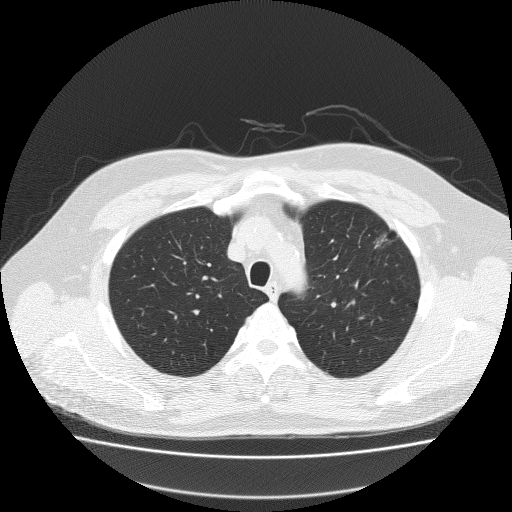
Low-dose screening chest CT, one axial slice. Slice 161 of 204 in the series (ordered by position). Reconstruction kernel FC51. 120 kVp. Lung window (W 1500 / L -600 HU). 2 mm slice thickness. 512 × 512 image matrix, field of view 410 × 410 mm.
Structures marked on this image (expert manual segmentation):
- lesion 1 (tumor, upper lobe of left lung): bounding box [x1, y1, x2, y2] px = [375, 232, 390, 245]